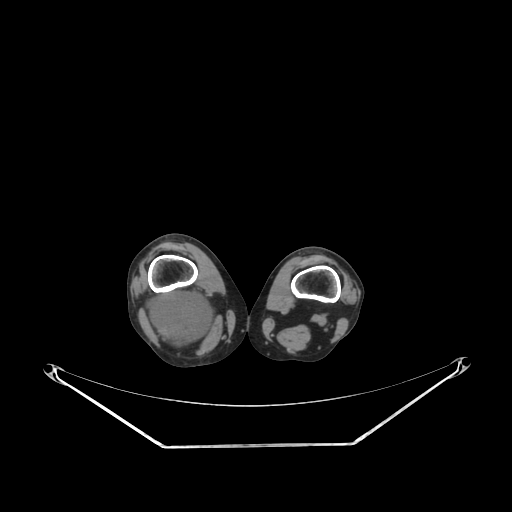
CT of an extremity soft-tissue mass (from a PET/CT study), one axial slice; position 181 of 267 along the scan axis; reconstruction kernel SOFT; soft-tissue window (W 400 / L 40 HU); 3.75 mm slice thickness; 512 × 512 image matrix, field of view 500 × 500 mm. Female patient. Case-level facts recorded for this patient, not image findings: histological type: liposarcoma; site of the primary tumour: right thigh.
Structures marked on this image (expert contour drawn on MRI and transferred to this co-registered scan by the dataset authors):
- gross tumour volume (mass): bounding box [x1, y1, x2, y2] px = [144, 290, 215, 350]